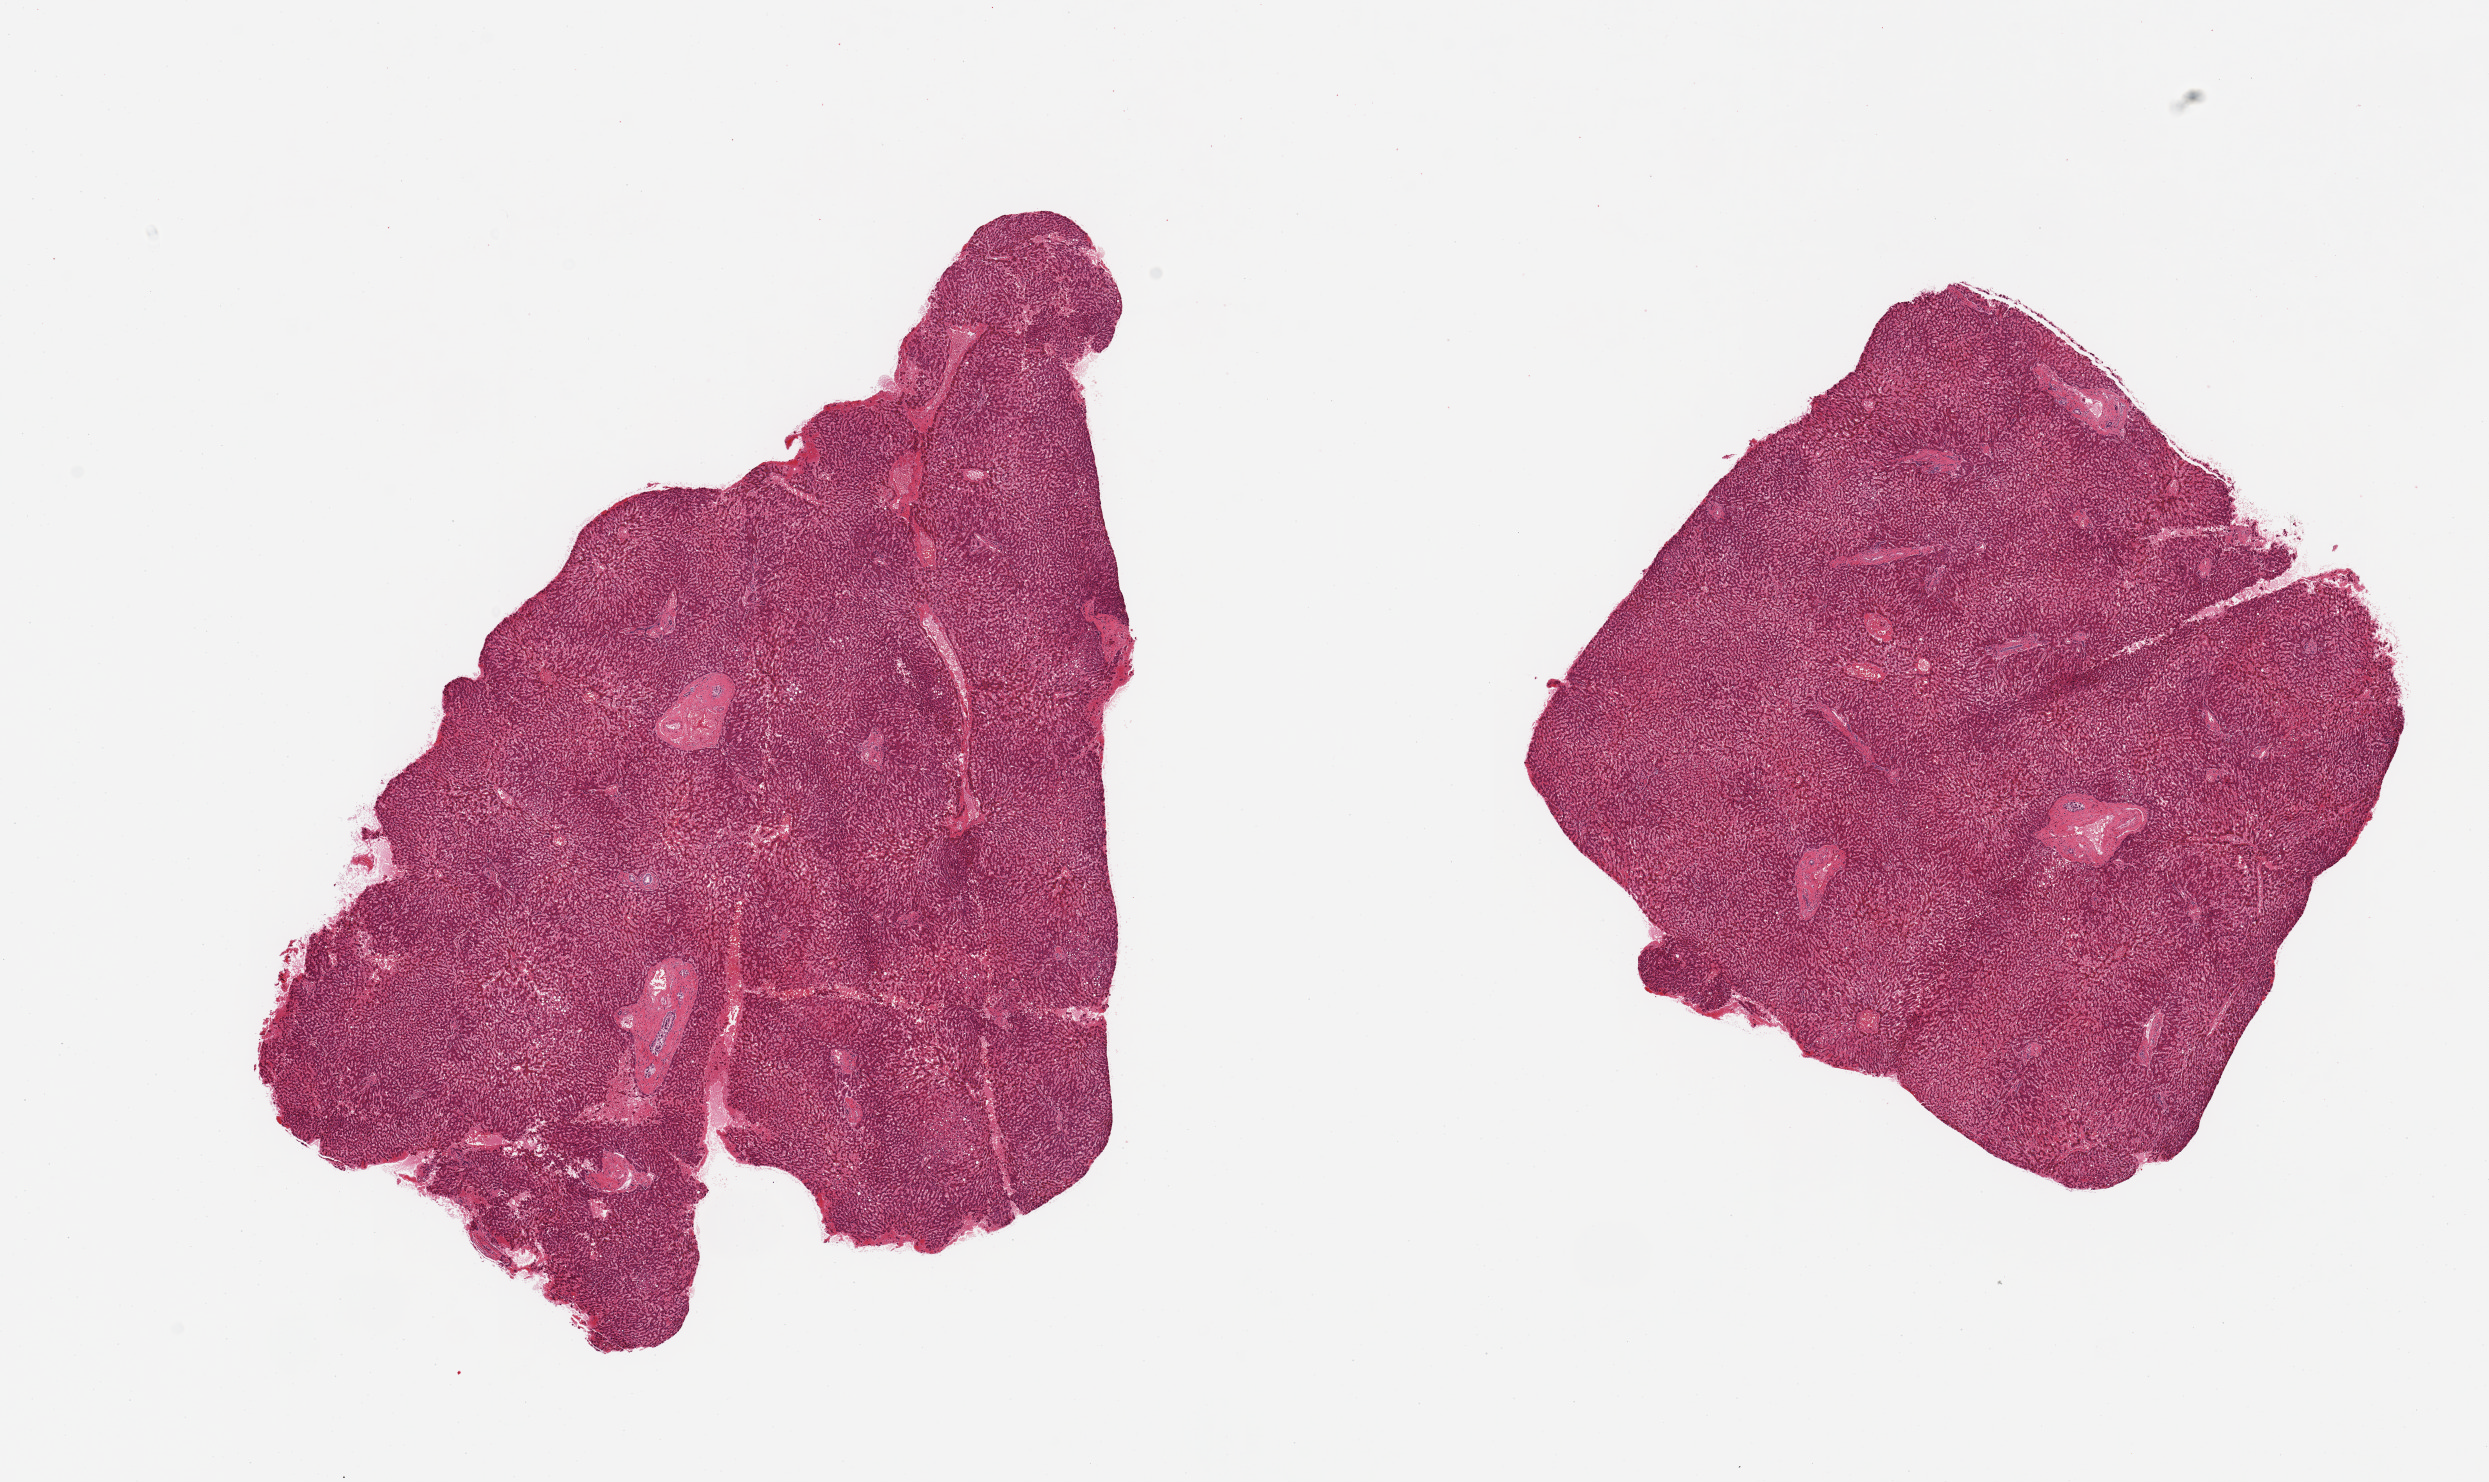
Digitized hematoxylin and eosin (H&E)-stained section, brightfield — a low-resolution overview of the entire scanned area, about 19.7 x 11.7 mm (slide scanned at 20x). PAXgene-fixed paraffin-embedded (PFPE) section. Sampled site (target tissue): liver. Donor tissue sample. Donor: female.
- pathologist's review note for this sample: 2 pieces; congestion and mild fatty change